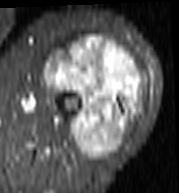
MRI of an extremity soft-tissue mass, one axial slice. Slice 59 of 103 in the series (ordered by position). STIR. MR volume resampled by the dataset authors to the PET/CT grid (not the native acquisition matrix). 3.27 mm slice thickness. 179 × 193 image matrix, field of view 175 × 188 mm. Female patient. From the clinical record (not read from this slice): histological type: undifferentiated – high grade; grade: high; site of the primary tumour: left thigh.
Outlined on this slice (expert contour drawn on MRI and transferred to this co-registered scan by the dataset authors):
- gross tumour volume including surrounding oedema: box from (x=43, y=37) to (x=142, y=161) px
- gross tumour volume (mass): (x=43, y=37)–(x=142, y=161)